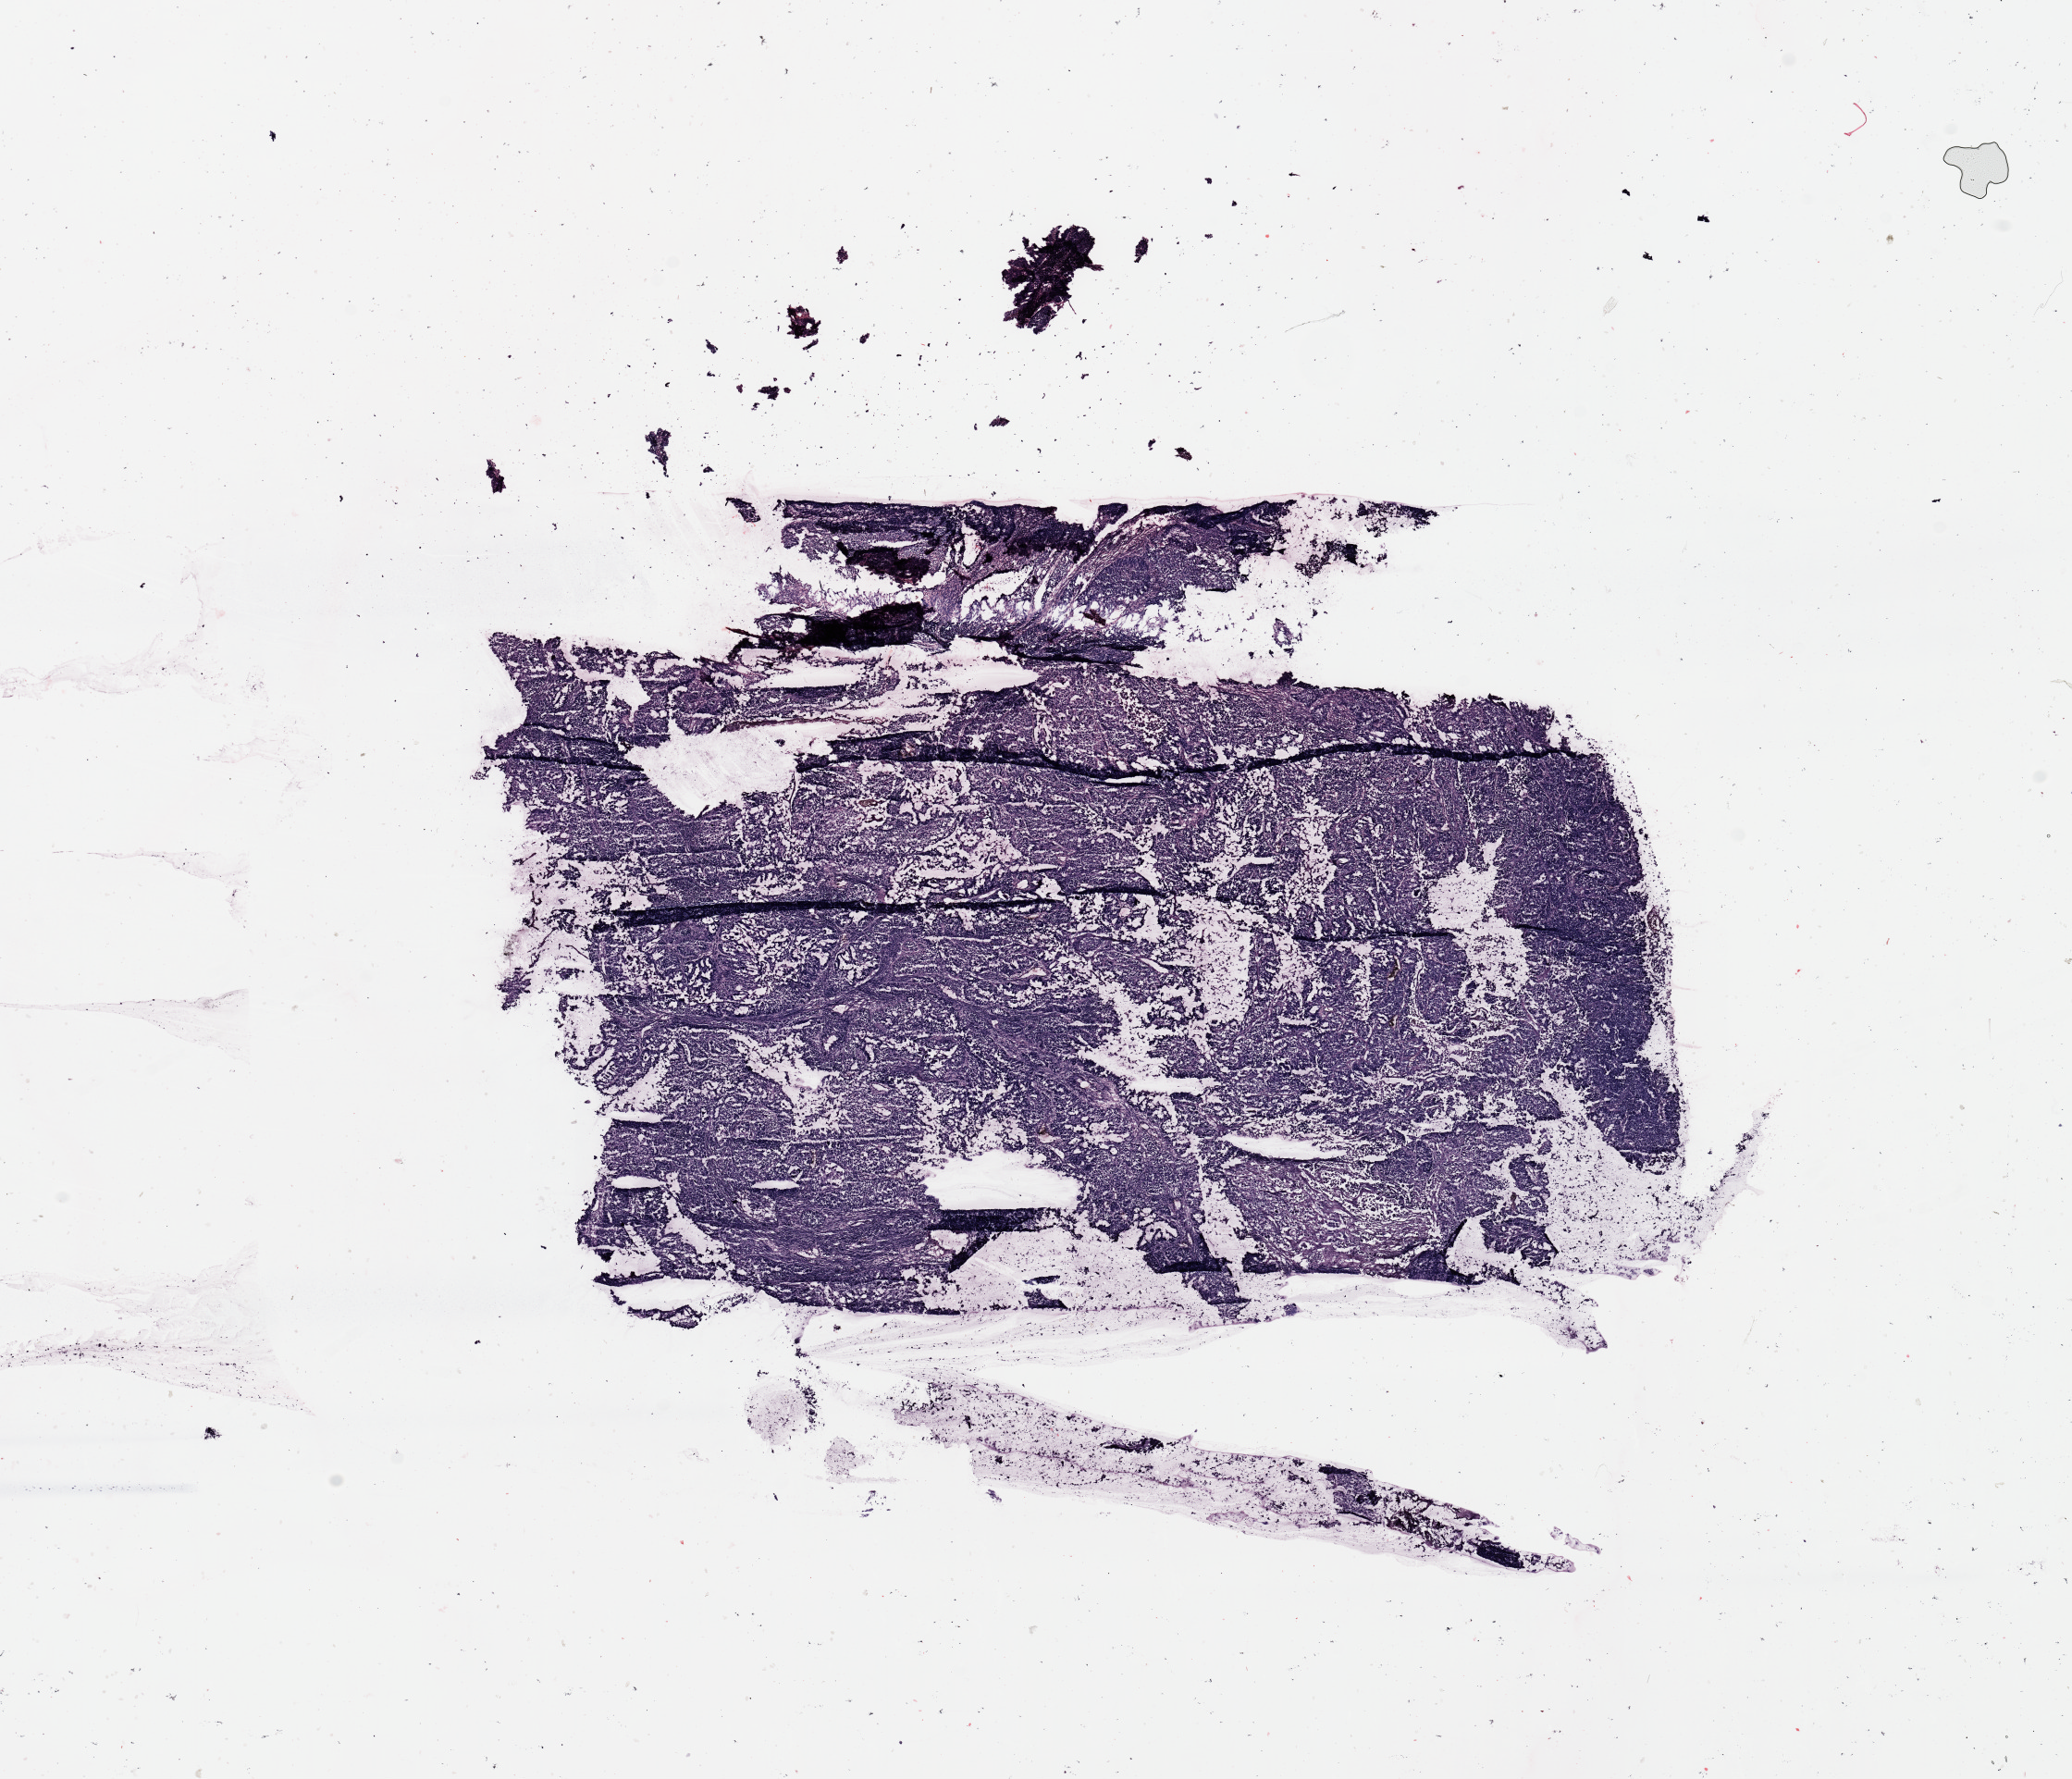
Digitized Hematoxylin and eosin (H&E) stained tissue section (whole slide), low-resolution overview of the scanned area, about 17.7 x 15.2 mm (from a 20x scan); uterus, tumour tissue. Patient: female, age 62 years. Histologic grade: G3 (poorly differentiated).
AJCC pathologic stage: I. Histologic diagnosis: Endometrioid adenocarcinoma, NOS.